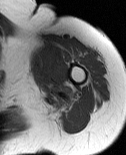
MRI of an extremity soft-tissue mass, one axial slice. Slice 62 of 86 in the series (ordered by position). MR volume resampled by the dataset authors to the PET/CT grid (not the native acquisition matrix). 126 × 155 image matrix, field of view 123 × 151 mm. Female patient. Case-level facts recorded for this patient, not image findings: histological type: pleiomorphic leiomyosarcoma; grade: high; site of the primary tumour: left biceps.
Annotated regions visible in this slice (expert contour drawn on MRI and transferred to this co-registered scan by the dataset authors):
- gross tumour volume including surrounding oedema: bounding box (x1, y1, x2, y2) in pixels: (29, 44, 62, 96)
- gross tumour volume (mass): (29, 47, 60, 82)